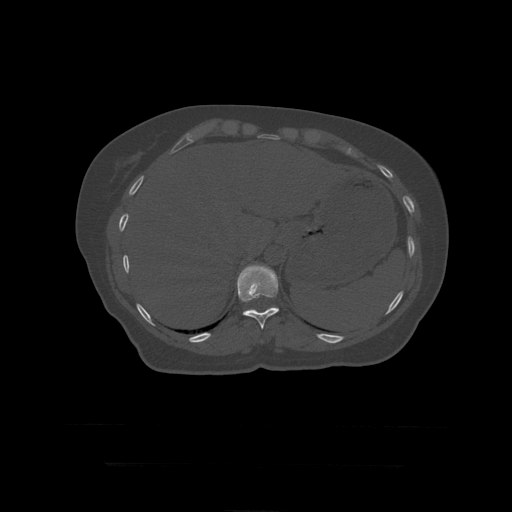
CT including the spine, one axial slice; position 216 of 399 along the scan axis; bone window (W 1800 / L 400 HU); 1.25 mm slice thickness; 512 × 512 image matrix, field of view 450 × 450 mm. Patient age 41 years. From the clinical record (not read from this slice): primary cancer: breast.
Annotated regions visible in this slice (semi-automatically segmented with operator editing):
- T11 vertebra: bounding box (x1, y1, x2, y2) in pixels: (237, 262, 280, 330)
- T12 vertebra: (246, 267, 279, 312)